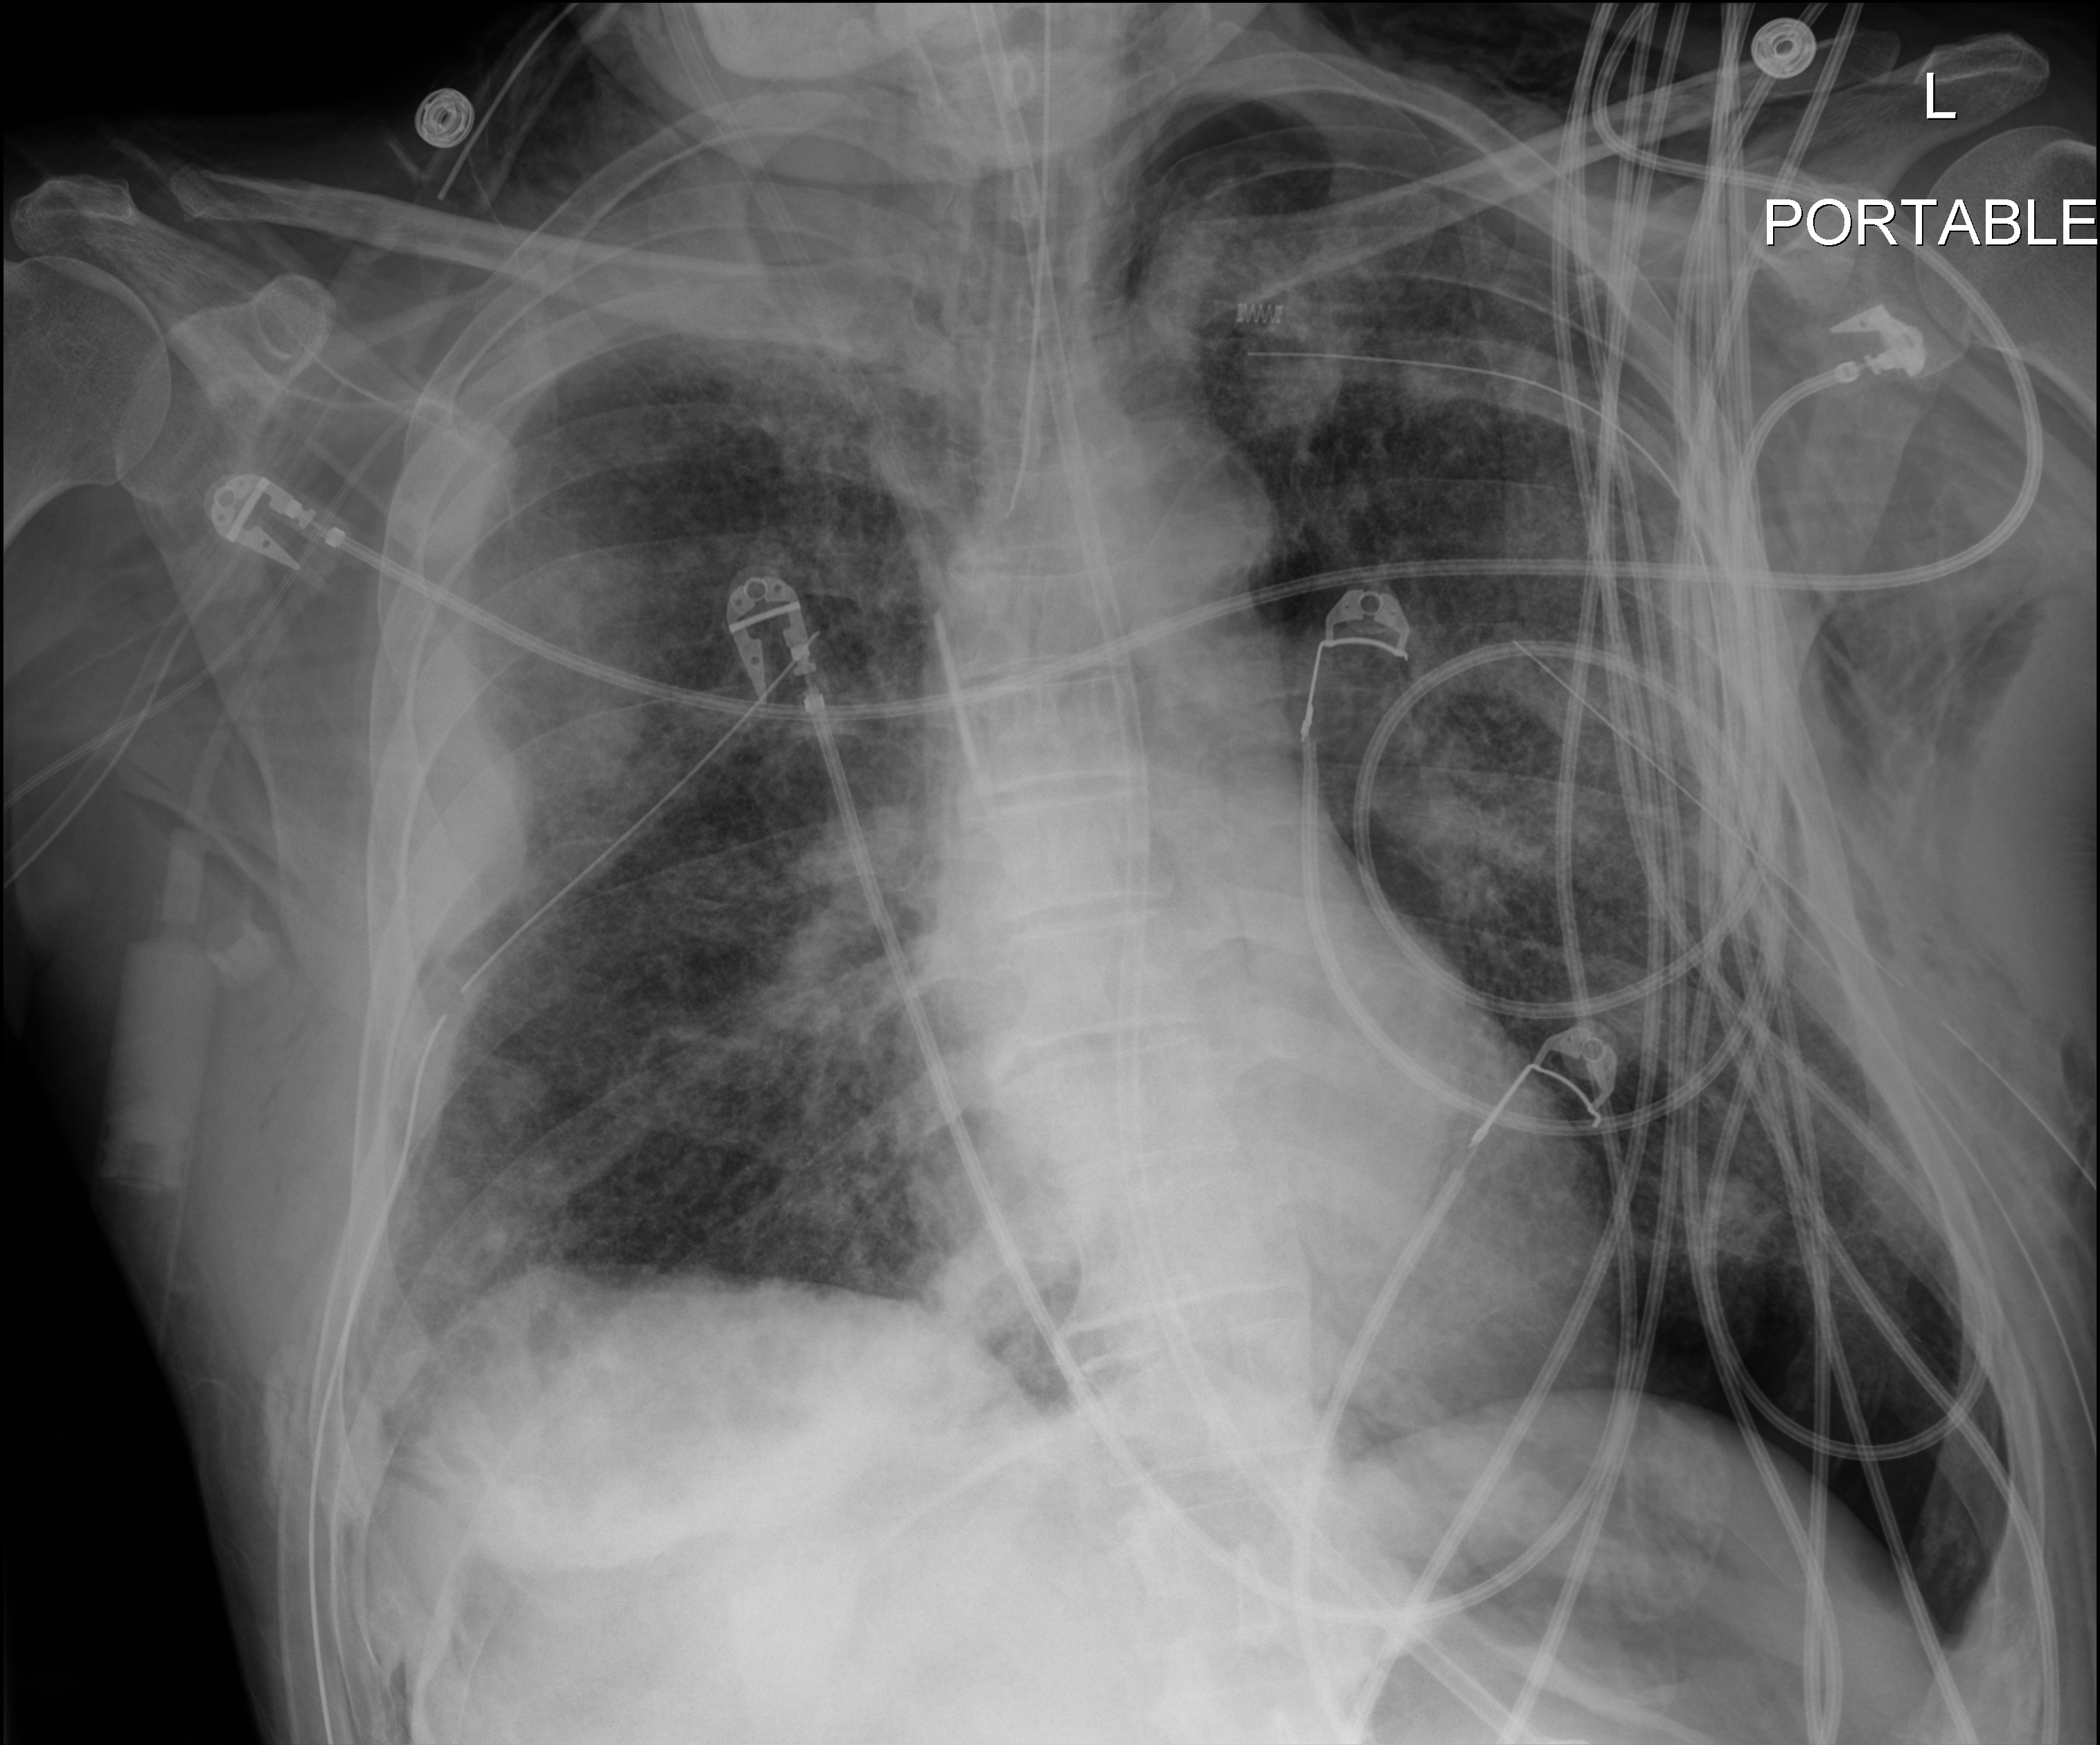
Bedside chest radiograph (digital radiography). Male patient hospitalised with COVID-19, age 18–59 years.
Hospital-stay facts (about this admission, not read from this image; timing relative to this image not recorded):
- diabetes (admission record): no
- mechanically ventilated during this hospital stay: yes
- admitted to intensive care during this hospital stay: yes